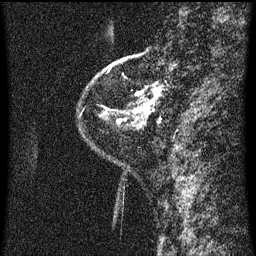
Breast MRI (dynamic contrast-enhanced), one sagittal slice; slice 8 of 60 in the series (ordered by position); dynamic contrast-enhanced series, image 2 of 3 at this slice position (ordered by acquisition); 1.5 T; TE 4.2 ms, TR 8 ms; 256 × 256 image matrix, field of view 180 × 180 mm. Female patient, age 48 years.
Structures marked on this image (semi-automatic segmentation, software-assisted and operator-edited):
- analysis volume of interest (the breast-tissue region the enhancement analysis was run in; not a lesion): bounding box [x1, y1, x2, y2] px = [128, 54, 175, 125]
- tumour enhancement mask (voxels above the 70 % enhancement threshold inside the analysis volume of interest): [132, 82, 162, 123]